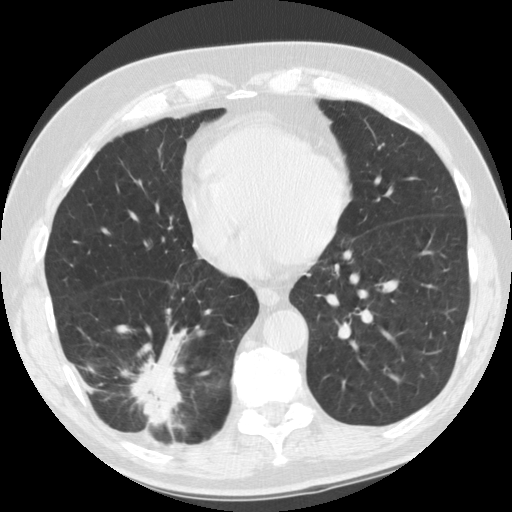
Low-dose screening chest CT, one axial slice. Slice 44 of 135 in the series (ordered by position). Lung window (W 1500 / L -600 HU). 2.5 mm slice thickness. 512 × 512 image matrix, field of view 340 × 340 mm.
Structures marked on this image (outlined manually by an expert reader):
- lesion 1 (tumor, lower lobe of right lung): bounding box (x1, y1, x2, y2) in pixels: (121, 356, 183, 430)